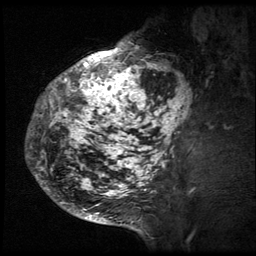
Breast MRI (dynamic contrast-enhanced), one sagittal slice. Slice 18 of 64 in the series (ordered by position). 3 images stored at this slice position (order not interpretable as contrast timing). 1.5 T. TE 4.2 ms, TR 9 ms. 2.5 mm slice thickness. 256 × 256 image matrix, field of view 180 × 180 mm. Patient: female, 50 years. From the clinical record (not read from this slice): setting: breast cancer imaged before/during neoadjuvant chemotherapy; receptor status: triple-negative.
Outlined on this slice (semi-automatically segmented with operator editing):
- analysis volume of interest (the breast-tissue region the enhancement analysis was run in; not a lesion): bounding box <25,39,194,212> (left, top, right, bottom; pixels)
- tumour enhancement mask (voxels above the 140 % enhancement threshold inside the analysis volume of interest): <26,39,194,212>